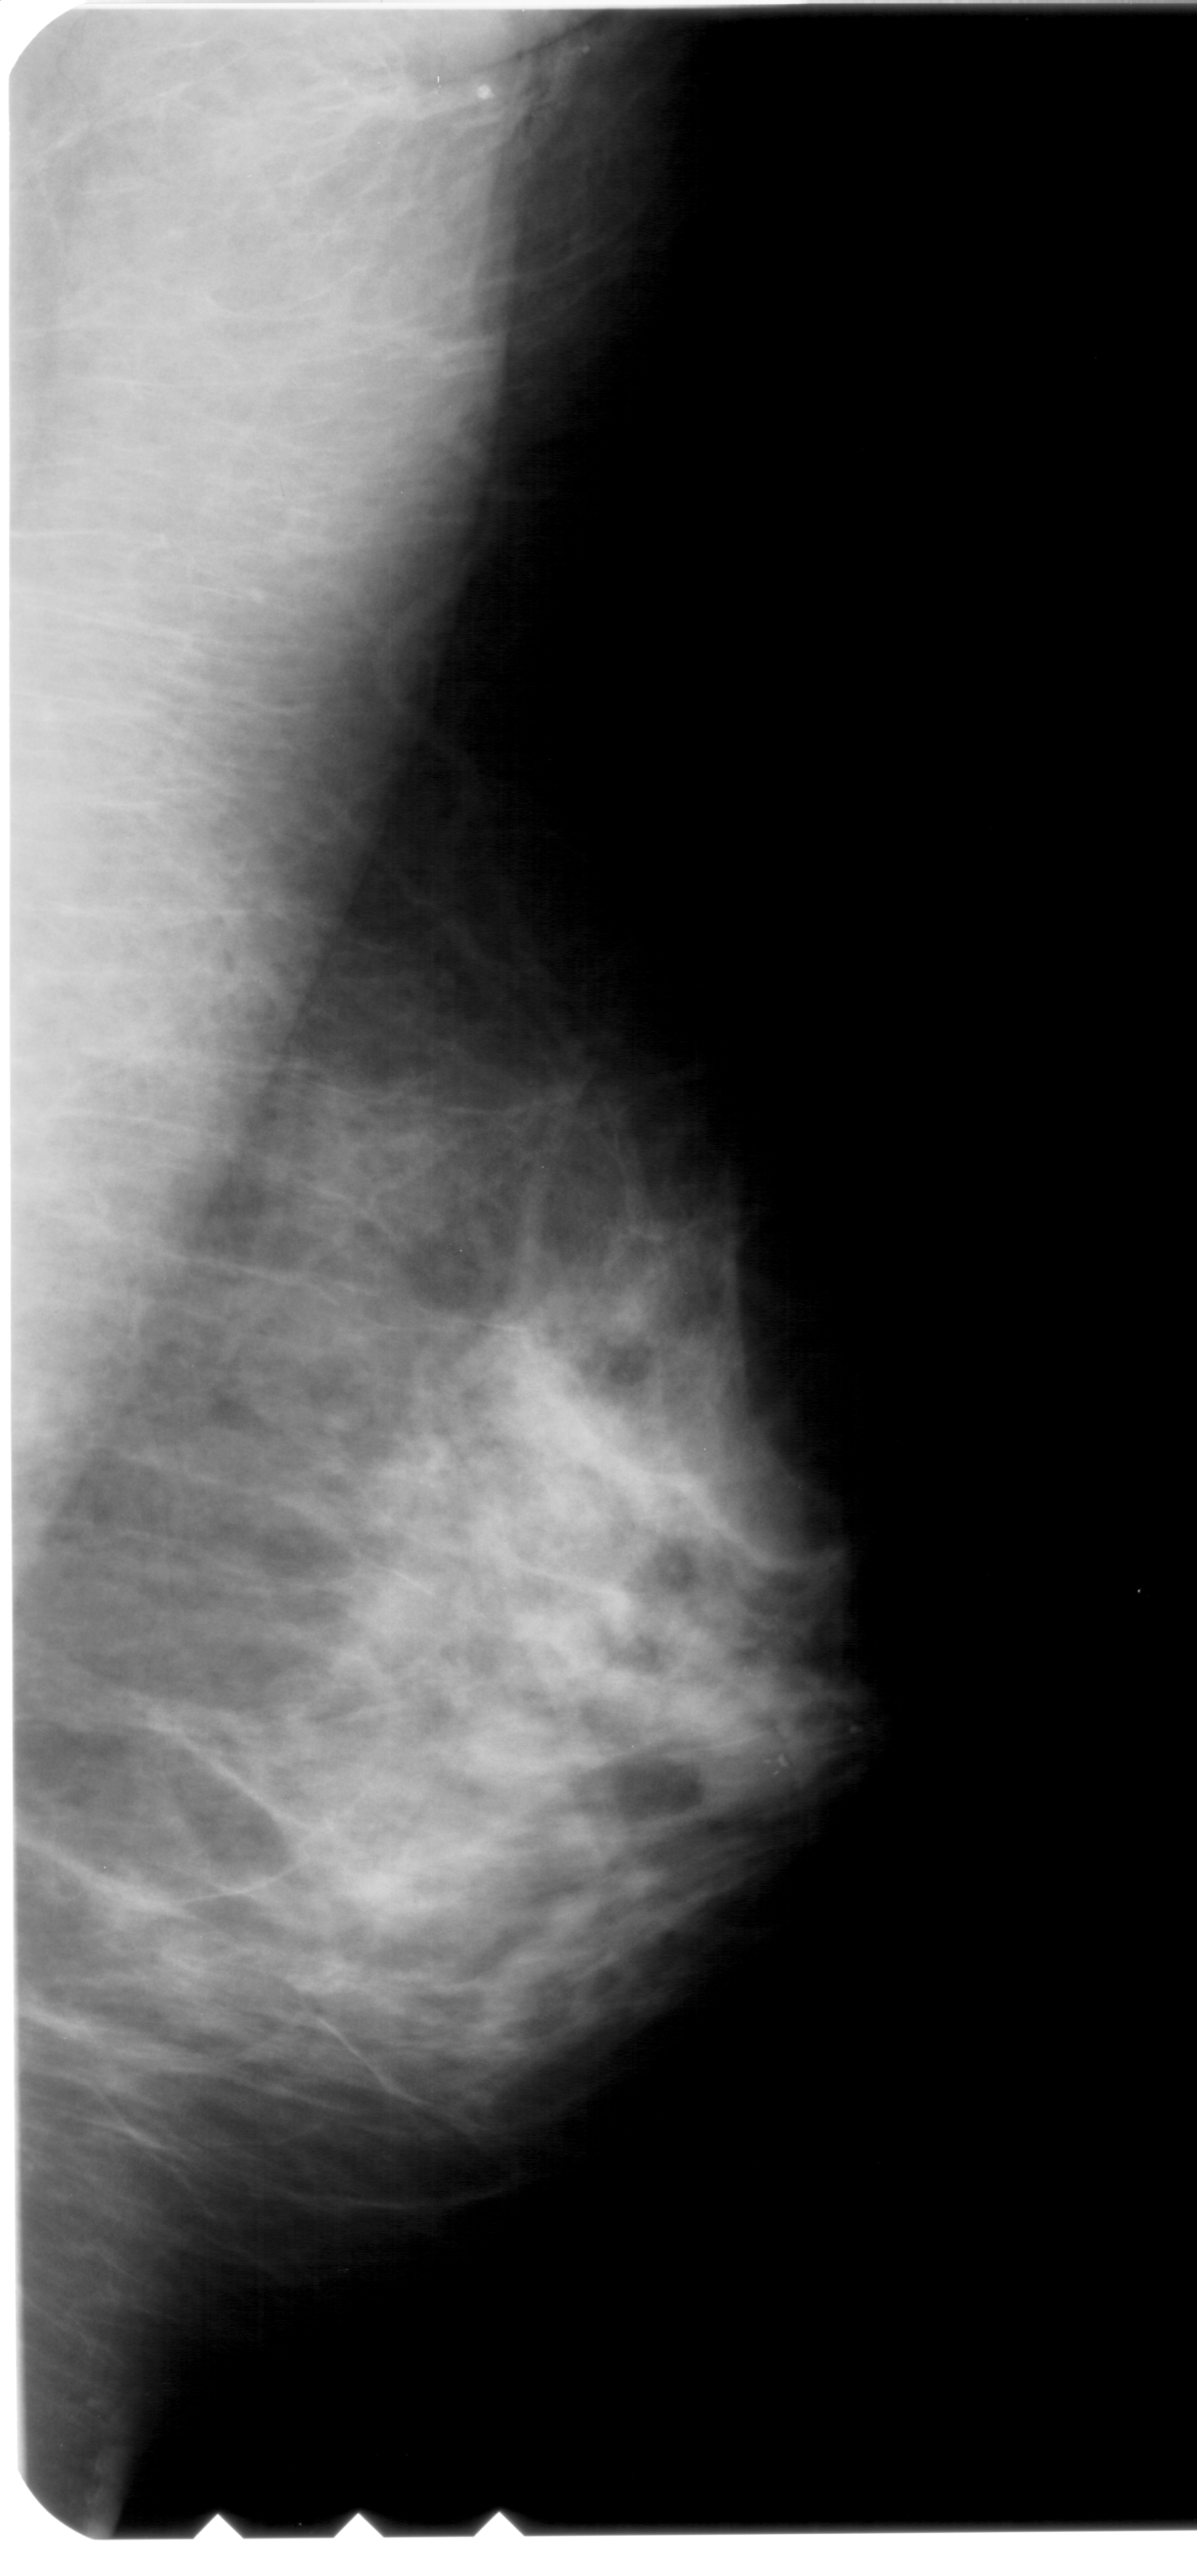
Scanned film-screen mammogram; right breast; MLO view; BI-RADS breast density category 4 (scale 1–4); 1197 × 2576 image matrix.
Expert-marked regions of interest on this film, with their recorded descriptors:
- calcifications, morphology amorphous, distribution clustered; BI-RADS assessment category 4; pathology (as recorded): benign: bounding box <643,1619,889,1853> (left, top, right, bottom; pixels)